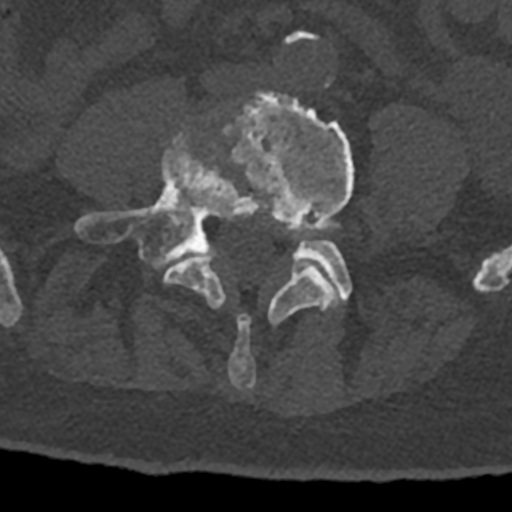
CT including the spine, one axial slice; position 230 of 797 along the scan axis; reconstruction kernel Br40s/3; bone window (W 1800 / L 400 HU); 0.5 mm slice thickness; 512 × 512 image matrix. Patient: male, 74 years. From the clinical record (not read from this slice): primary cancer: renal.
Outlined on this slice (semi-automatic segmentation, software-assisted and operator-edited):
- L4 vertebra: bounding box (x1, y1, x2, y2) in pixels: (163, 91, 354, 390)
- L5 vertebra: (75, 134, 352, 301)